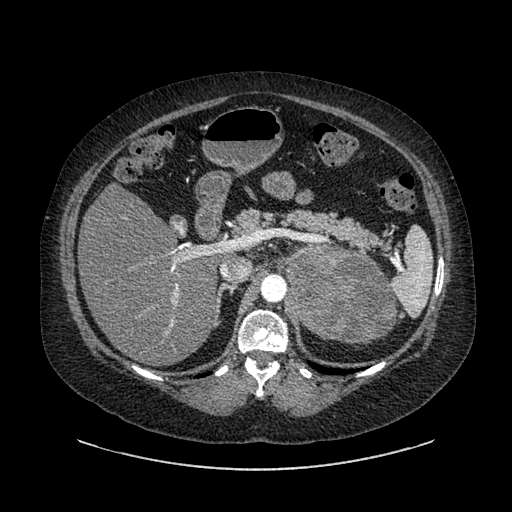
Contrast-enhanced abdominal CT, one axial slice; position 578 of 769 along the scan axis; reconstruction kernel SOFT; soft-tissue window (W 400 / L 40 HU); 0.62 mm slice thickness; 512 × 512 image matrix, field of view 460 × 460 mm. Female patient, age 61 years. From the clinical record (not read from this slice): diagnosis: adrenocortical carcinoma; tumour side: left adrenal; tumour size at pathology: 13 cm; Ki-67 index: 79 %; stage (as recorded): 2.
Structures marked on this image (semi-automatically segmented with operator editing):
- mass: box from (x=285, y=245) to (x=393, y=343) px